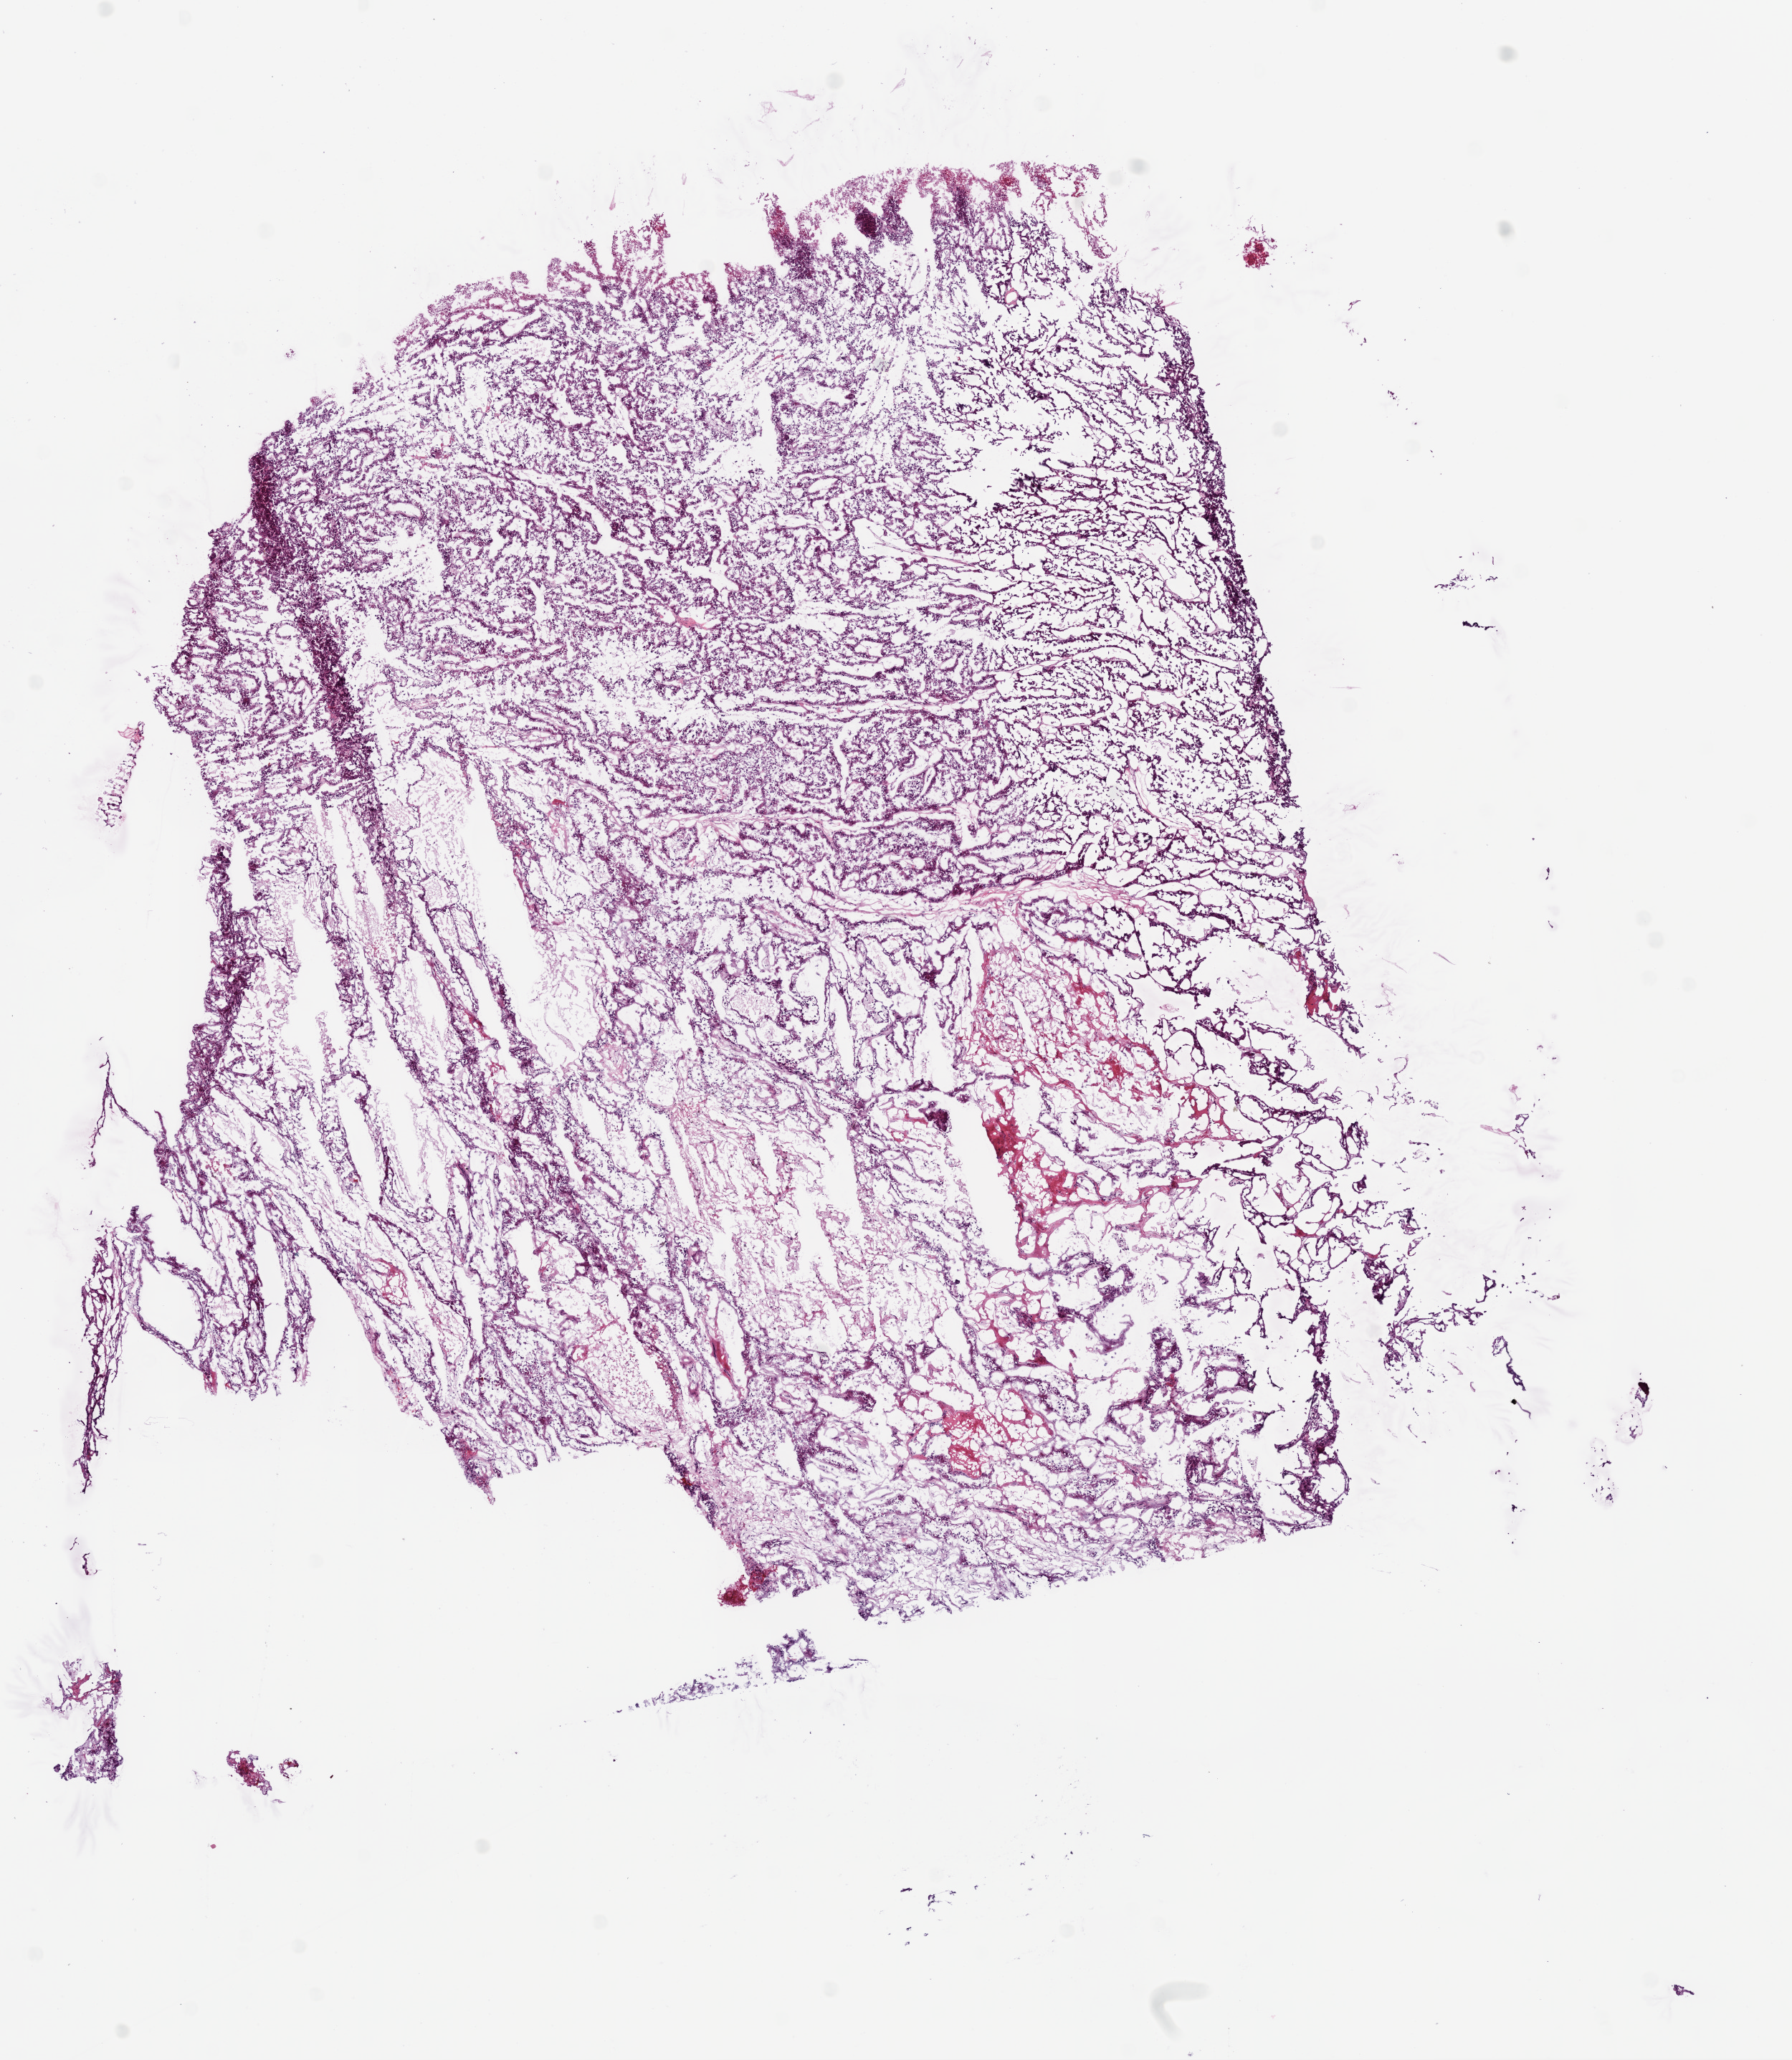
Digitized H&E tissue section (whole slide) — shown as a low-resolution overview of the whole scanned area (about 10.0 x 11.5 mm); frozen section from the bottom of the tissue portion; primary tumour sample from the kidney. Male patient; age at initial diagnosis 48 years. Histologic grade: G3 (poorly differentiated). Slide review estimates, as recorded: tumour cells 80%, tumour nuclei 76%, normal cells 0%, stromal cells 10%, necrosis 10%.
AJCC pathologic stage: II. Histologic diagnosis: Clear cell adenocarcinoma, NOS. Lymph nodes positive (case pathology): 0 of 1 examined.